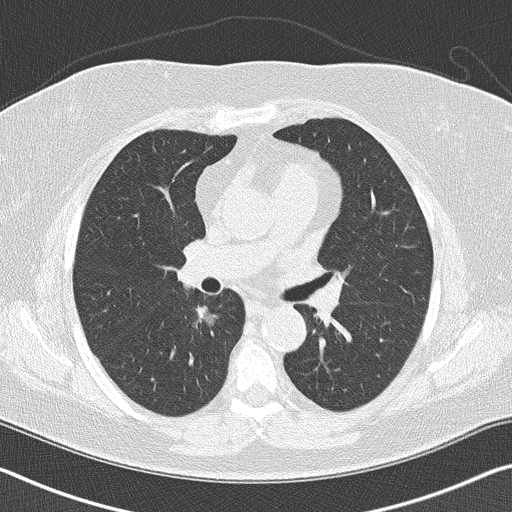
Low-dose screening chest CT, axial slice. Baseline annual screen. Lung window (W 1500 / L -600 HU). 2 mm slice thickness. Slice 60 of 146 in the series. Female participant, aged 60 years at enrolment. Former smoker at enrolment.
Expert-annotated lung lesion, bounding box (x1, y1, x2, y2) in pixels: (171, 293, 227, 344). The screening reader recorded 2 non-calcified nodules or masses ≥4 mm on this exam; which of them this box marks is not recorded. Official screen result: positive, change unspecified: nodule(s) >= 4 mm or enlarging nodule(s), mass(es), or other non-specific abnormalities suspicious for lung cancer.